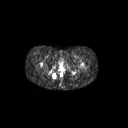
FDG PET of an extremity soft-tissue mass (from a PET/CT study), one axial slice; slice 33 of 267 in the series (ordered by position); 128 × 128 image matrix, field of view 700 × 700 mm. Patient: female, 17 years. Case-level facts recorded for this patient, not image findings: histological type: epithelioid sarcoma; grade: intermediate; site of the primary tumour: right buttock.
Structures marked on this image (expert contour drawn on MRI and transferred to this co-registered scan by the dataset authors):
- gross tumour volume including surrounding oedema: bounding box [x1, y1, x2, y2] px = [50, 71, 58, 80]
- gross tumour volume (mass): [51, 72, 57, 79]